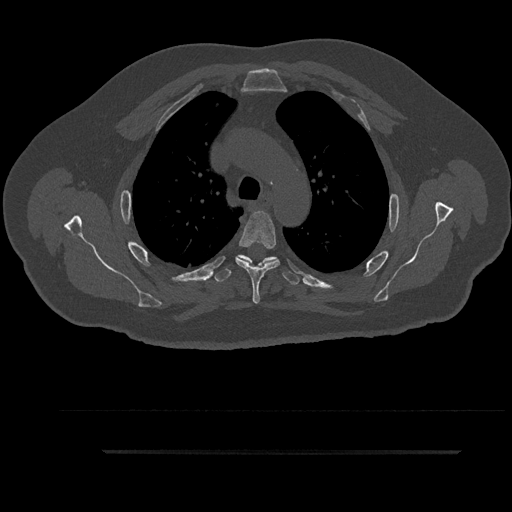
CT including the spine, one axial slice. Slice 663 of 797 in the series (ordered by position). 120 kVp. Bone window (W 1800 / L 400 HU). 0.5 mm slice thickness. 512 × 512 image matrix, field of view 432 × 432 mm. Male patient, age 63 years. From the clinical record (not read from this slice): primary cancer: renal.
Outlined on this slice (semi-automatic segmentation, software-assisted and operator-edited):
- T4 vertebra: bounding box (x1, y1, x2, y2) in pixels: (235, 211, 280, 304)
- T5 vertebra: (214, 254, 300, 285)